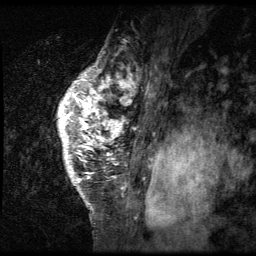
Breast MRI (dynamic contrast-enhanced), one sagittal slice; position 49 of 64 along the scan axis; 3 images stored at this slice position (order not interpretable as contrast timing); 1.5 T; TE 4.2 ms, TR 9 ms; 2.5 mm slice thickness; 256 × 256 image matrix, field of view 180 × 180 mm. Female patient, age 50 years. Case-level facts recorded for this patient, not image findings: setting: breast cancer imaged before/during neoadjuvant chemotherapy; receptor status: triple-negative.
Structures marked on this image (semi-automatically segmented with operator editing):
- analysis volume of interest (the breast-tissue region the enhancement analysis was run in; not a lesion): bounding box <32,39,138,212> (left, top, right, bottom; pixels)
- tumour enhancement mask (voxels above the 140 % enhancement threshold inside the analysis volume of interest): <57,70,138,206>